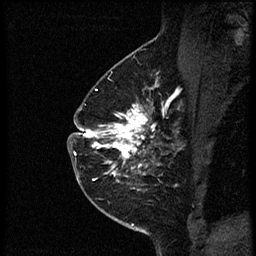
Breast MRI (dynamic contrast-enhanced), one sagittal slice. Position 38 of 56 along the scan axis. Dynamic contrast-enhanced study with each time point stored as its own series, time point 2 of 4 at this slice position (early post-contrast, ordered by acquisition time). 1.5 T. TE 4.2 ms, TR 18.9 ms. 256 × 256 image matrix. Female patient. From the clinical record (not read from this slice): setting: breast cancer imaged before/during neoadjuvant chemotherapy; receptor status: HER2-positive.
Outlined on this slice (semi-automatic segmentation, software-assisted and operator-edited):
- analysis volume of interest (the breast-tissue region the enhancement analysis was run in; not a lesion): box from (x=78, y=85) to (x=174, y=189) px
- tumour enhancement mask (voxels above the 100 % enhancement threshold inside the analysis volume of interest): (x=78, y=85)–(x=165, y=182)